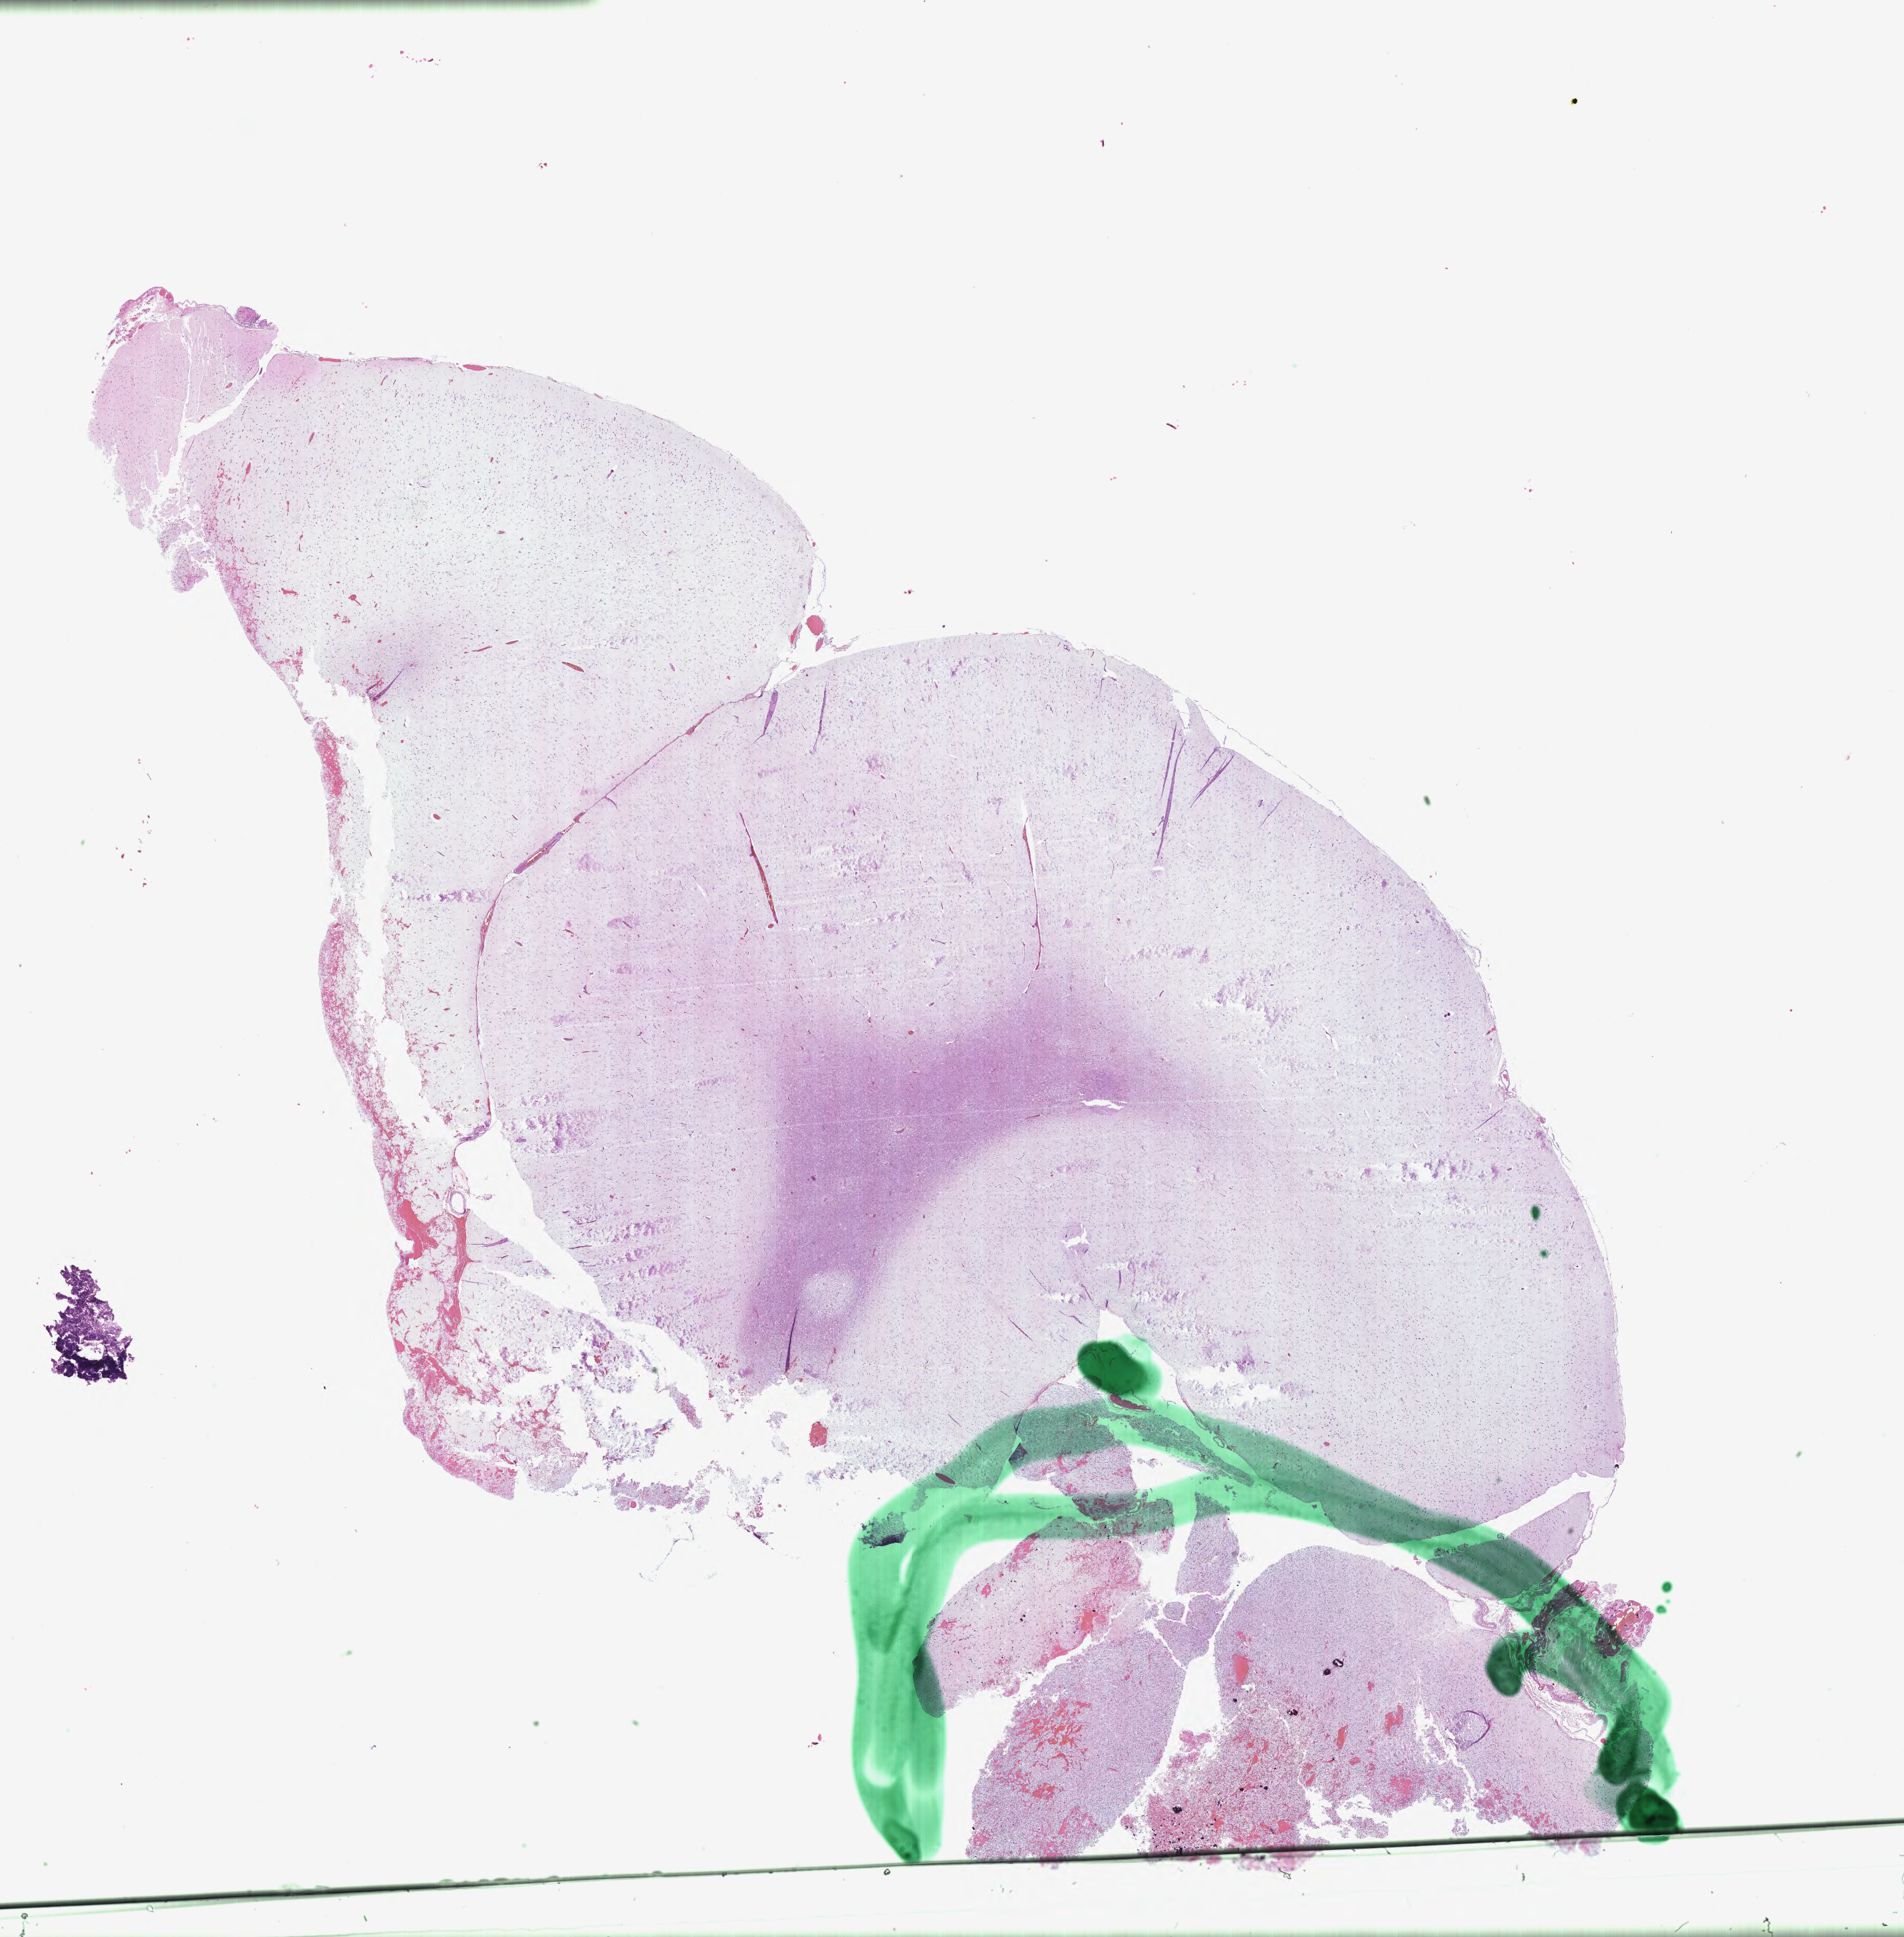
Whole-slide image, haematoxylin and eosin stain of tumor tissue from the brain, low-resolution overview of the scanned area, about 23.1 x 23.6 mm; formalin-fixed paraffin-embedded section. Female patient, age 148 months.
Diagnosis: Neuroepithelioma, NOS.